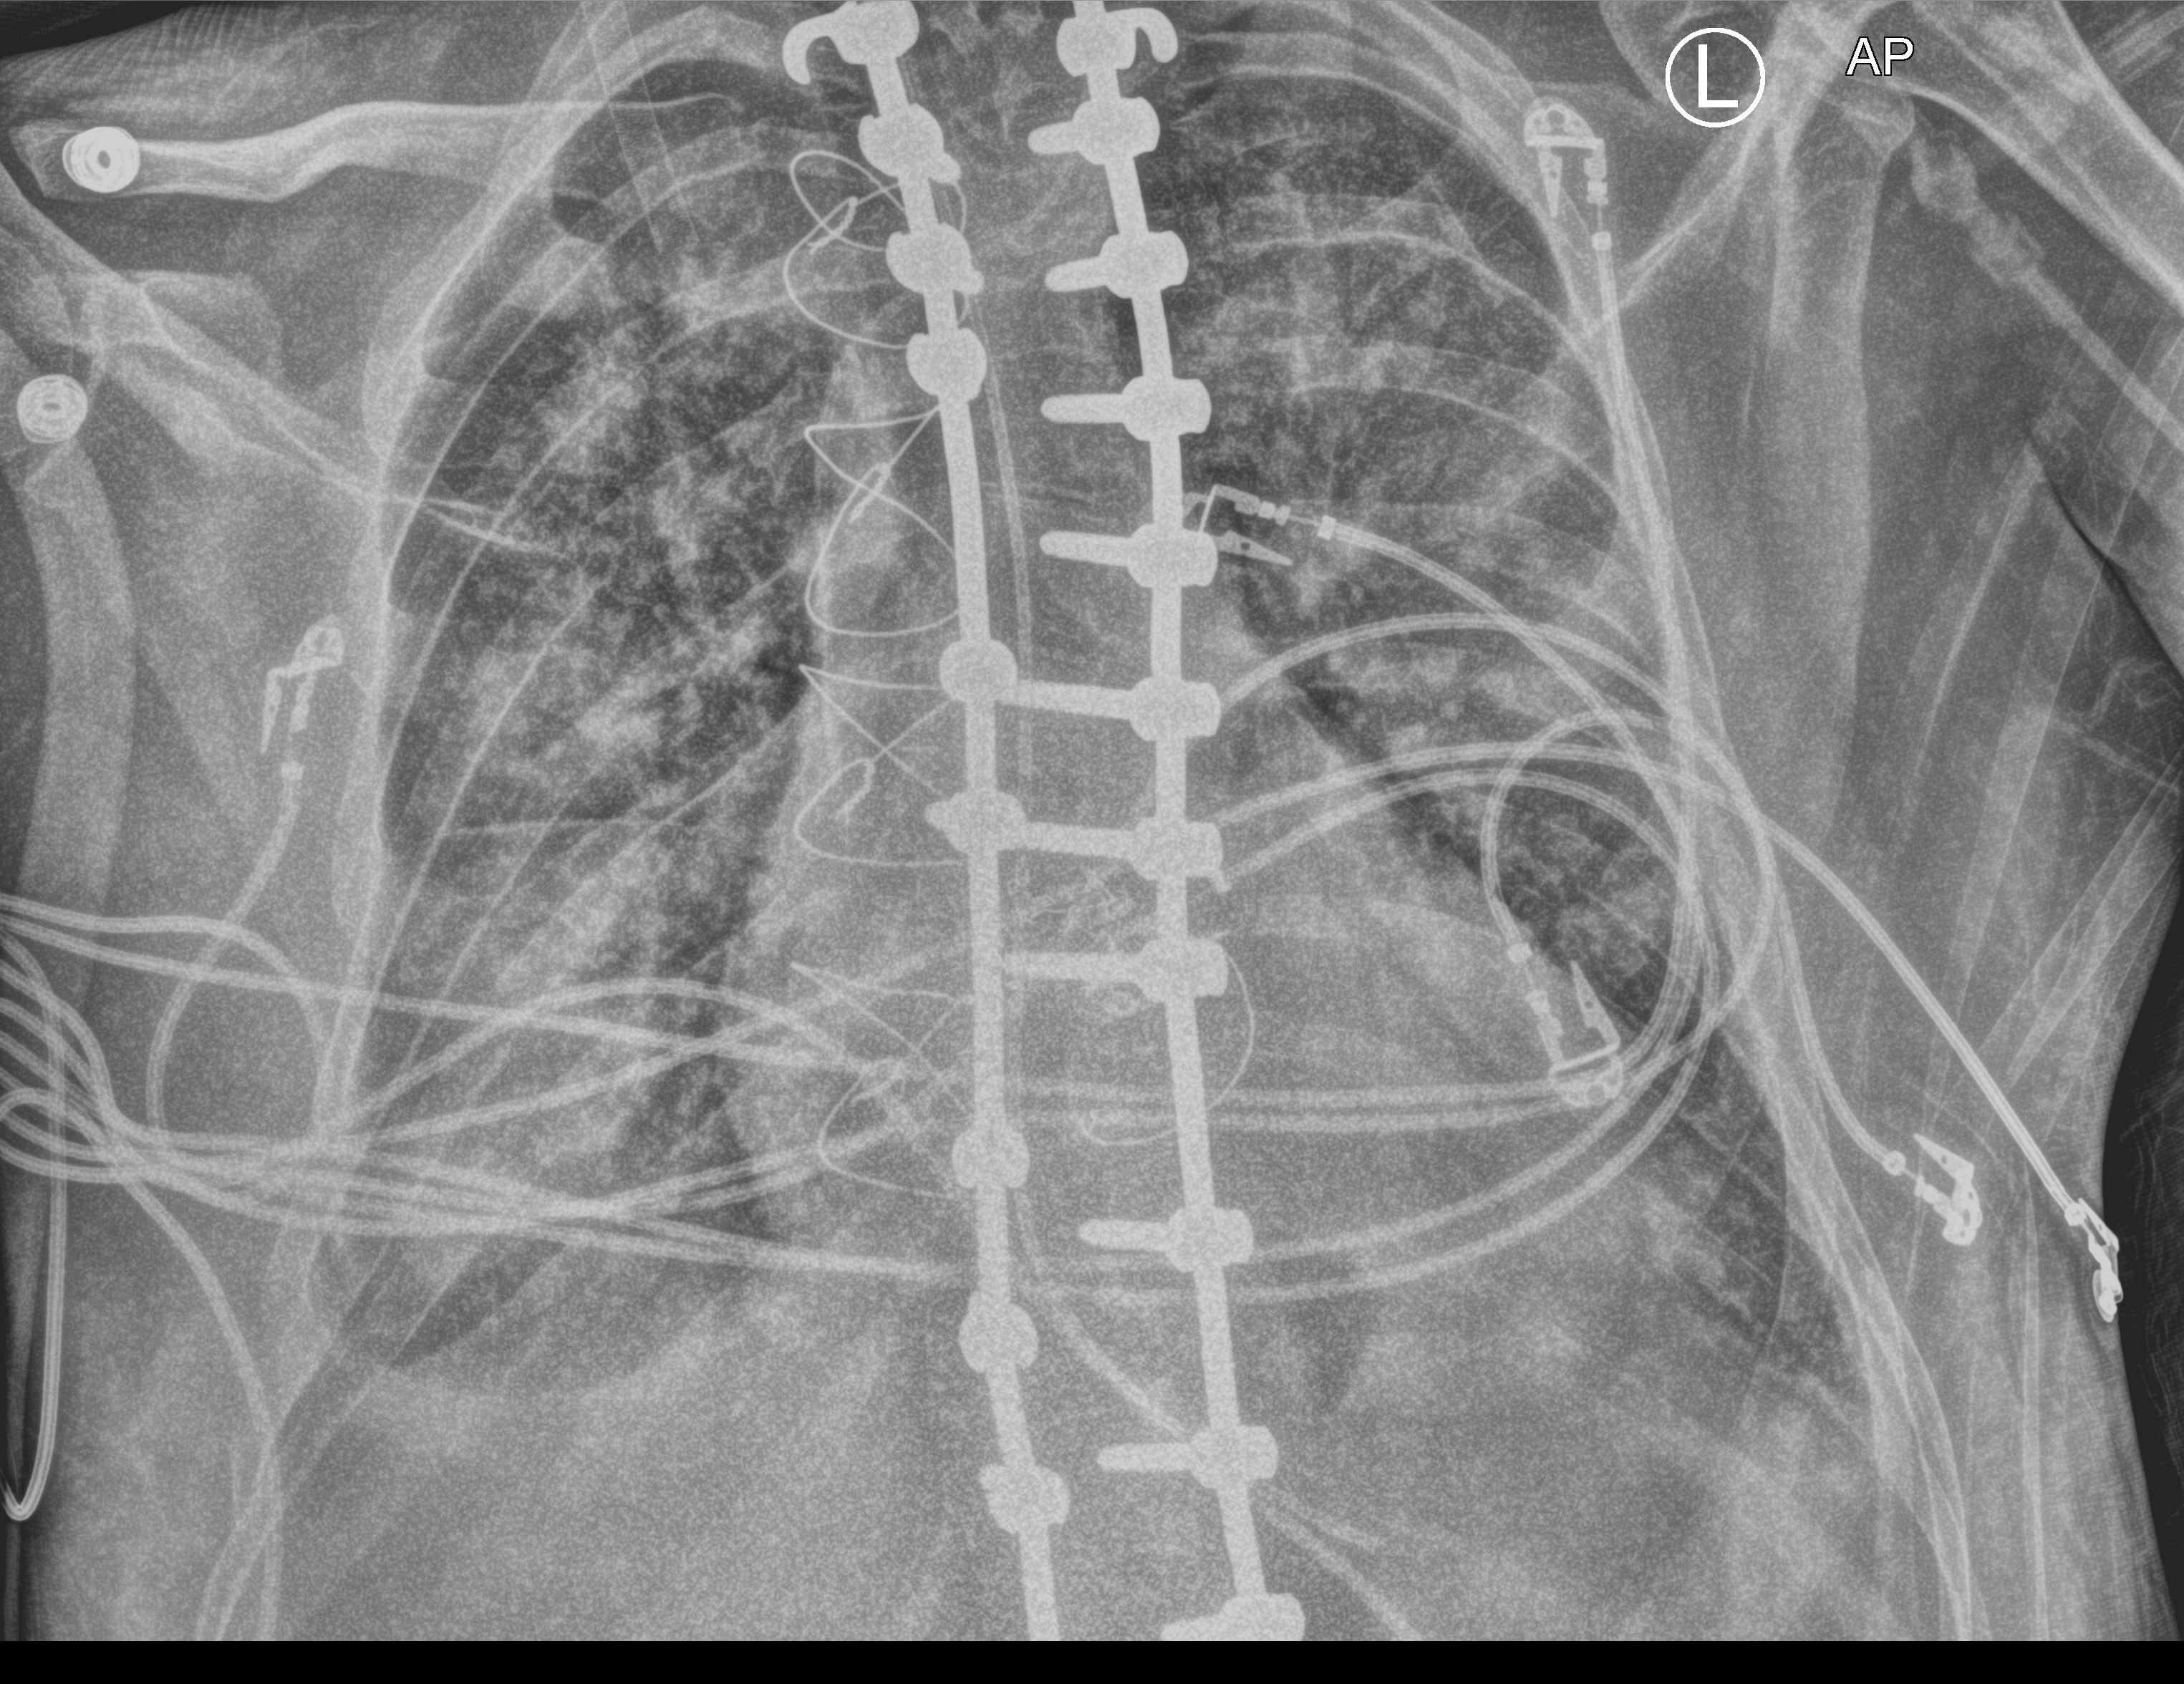
Bedside chest radiograph (computed radiography); anteroposterior (AP) projection. Adult patient hospitalised with COVID-19, age 18–59 years.
Hospital-stay facts (about this admission, not read from this image; timing relative to this image not recorded):
- admitted to intensive care during this hospital stay: yes
- hypertension (admission record): no